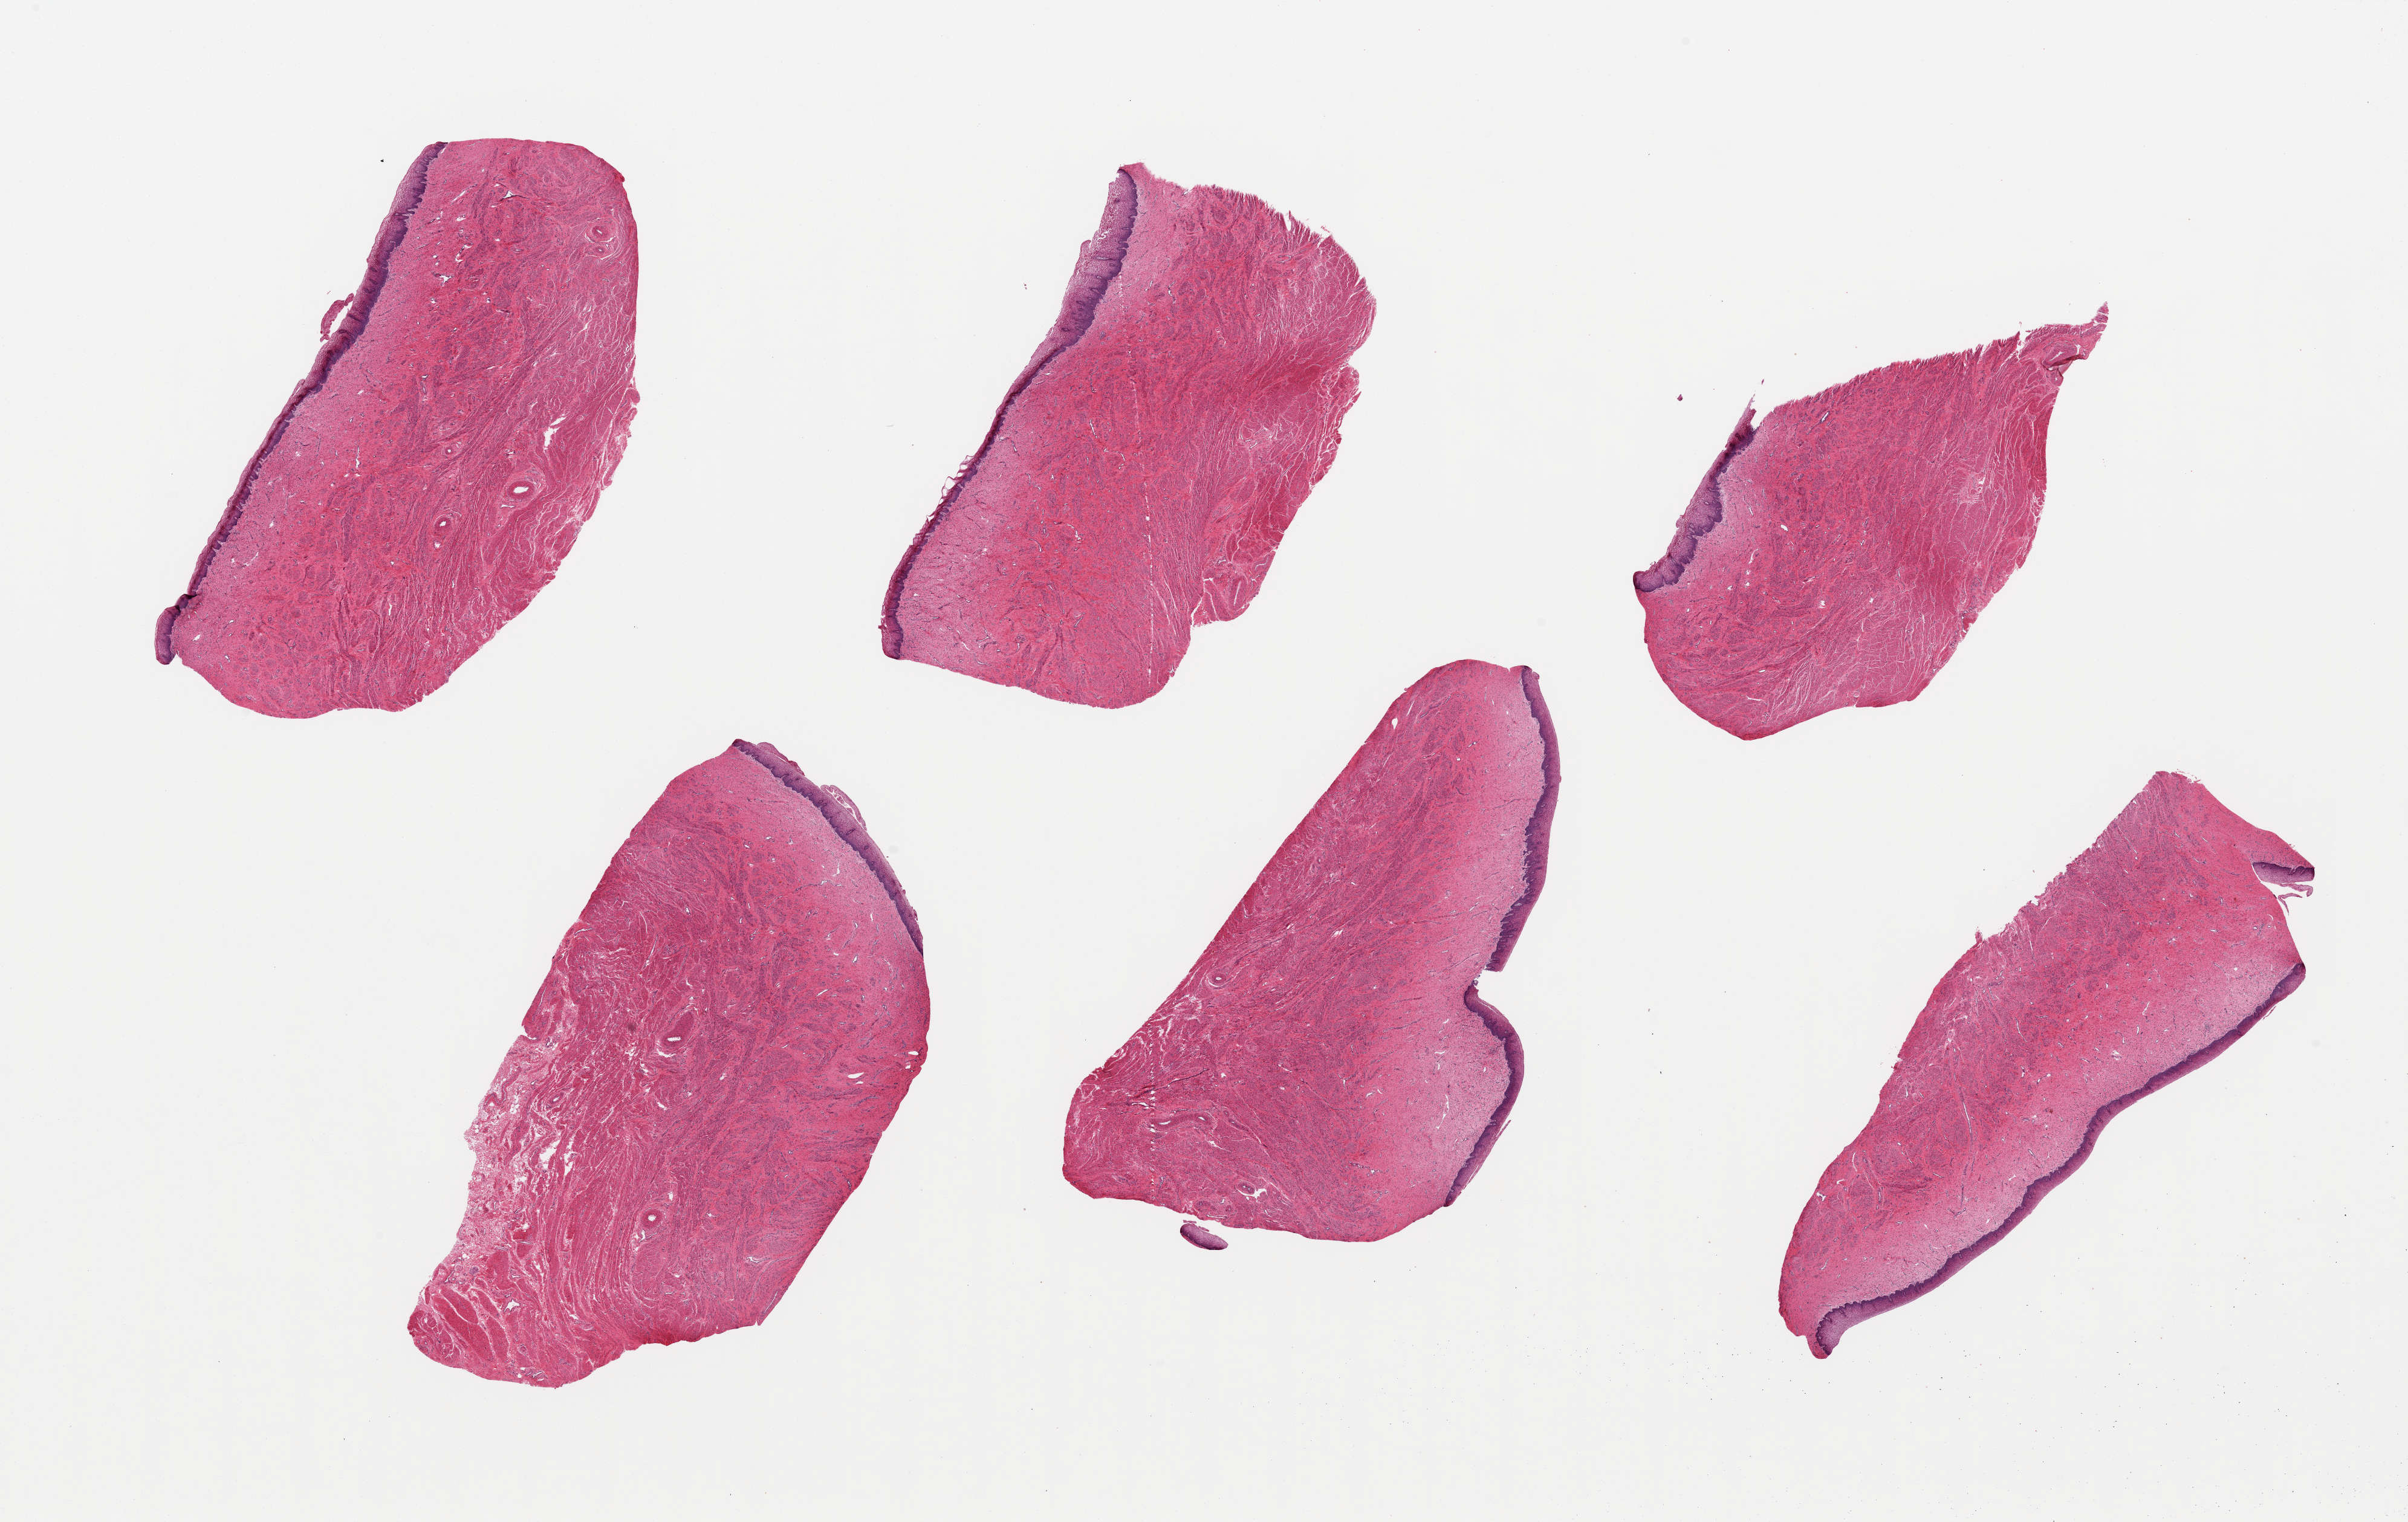
Whole-slide image, H&E stain, brightfield — a low-resolution overview of the entire scanned area, about 31.5 x 19.9 mm (acquisition: 20x scan), PAXgene-fixed, paraffin-embedded tissue, target tissue: vagina, tissue donor sample. Donor: female.
Review note (as recorded): 6 pieces, up to 9x5mm; all have epithelium.